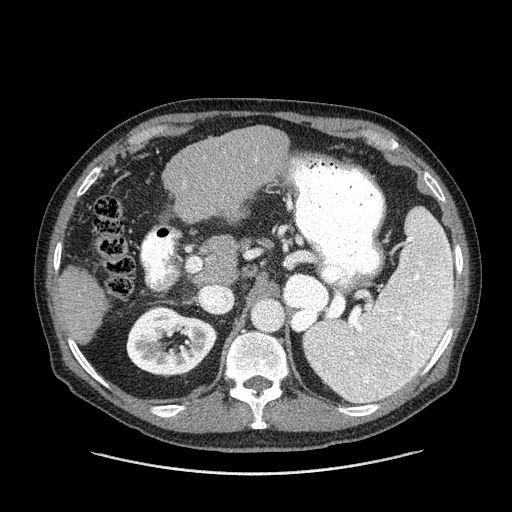
Contrast-enhanced abdominal CT (liver protocol), one axial slice; position 76 of 180 along the scan axis; 120 kVp; one of 2 acquisitions stored at this slice position; soft-tissue window (W 400 / L 40 HU); 2.5 mm slice thickness; 512 × 512 image matrix, field of view 420 × 420 mm. From the clinical record (not read from this slice): diagnosis: hepatocellular carcinoma (patient treated with transarterial chemoembolisation; whether this scan precedes or follows treatment is not stated here); TNM stage (as recorded): Stage-II; Child-Pugh class: A; tumour differentiation: well differentiated; tumour nodularity: multinodular.
Outlined on this slice (semi-automatically segmented with operator editing):
- liver parenchyma outside the tumour (the mass and vessels are separate outlines, so this box may not span the whole liver): bounding box [x1, y1, x2, y2] px = [56, 126, 290, 344]
- liver vessels: [255, 159, 257, 161]